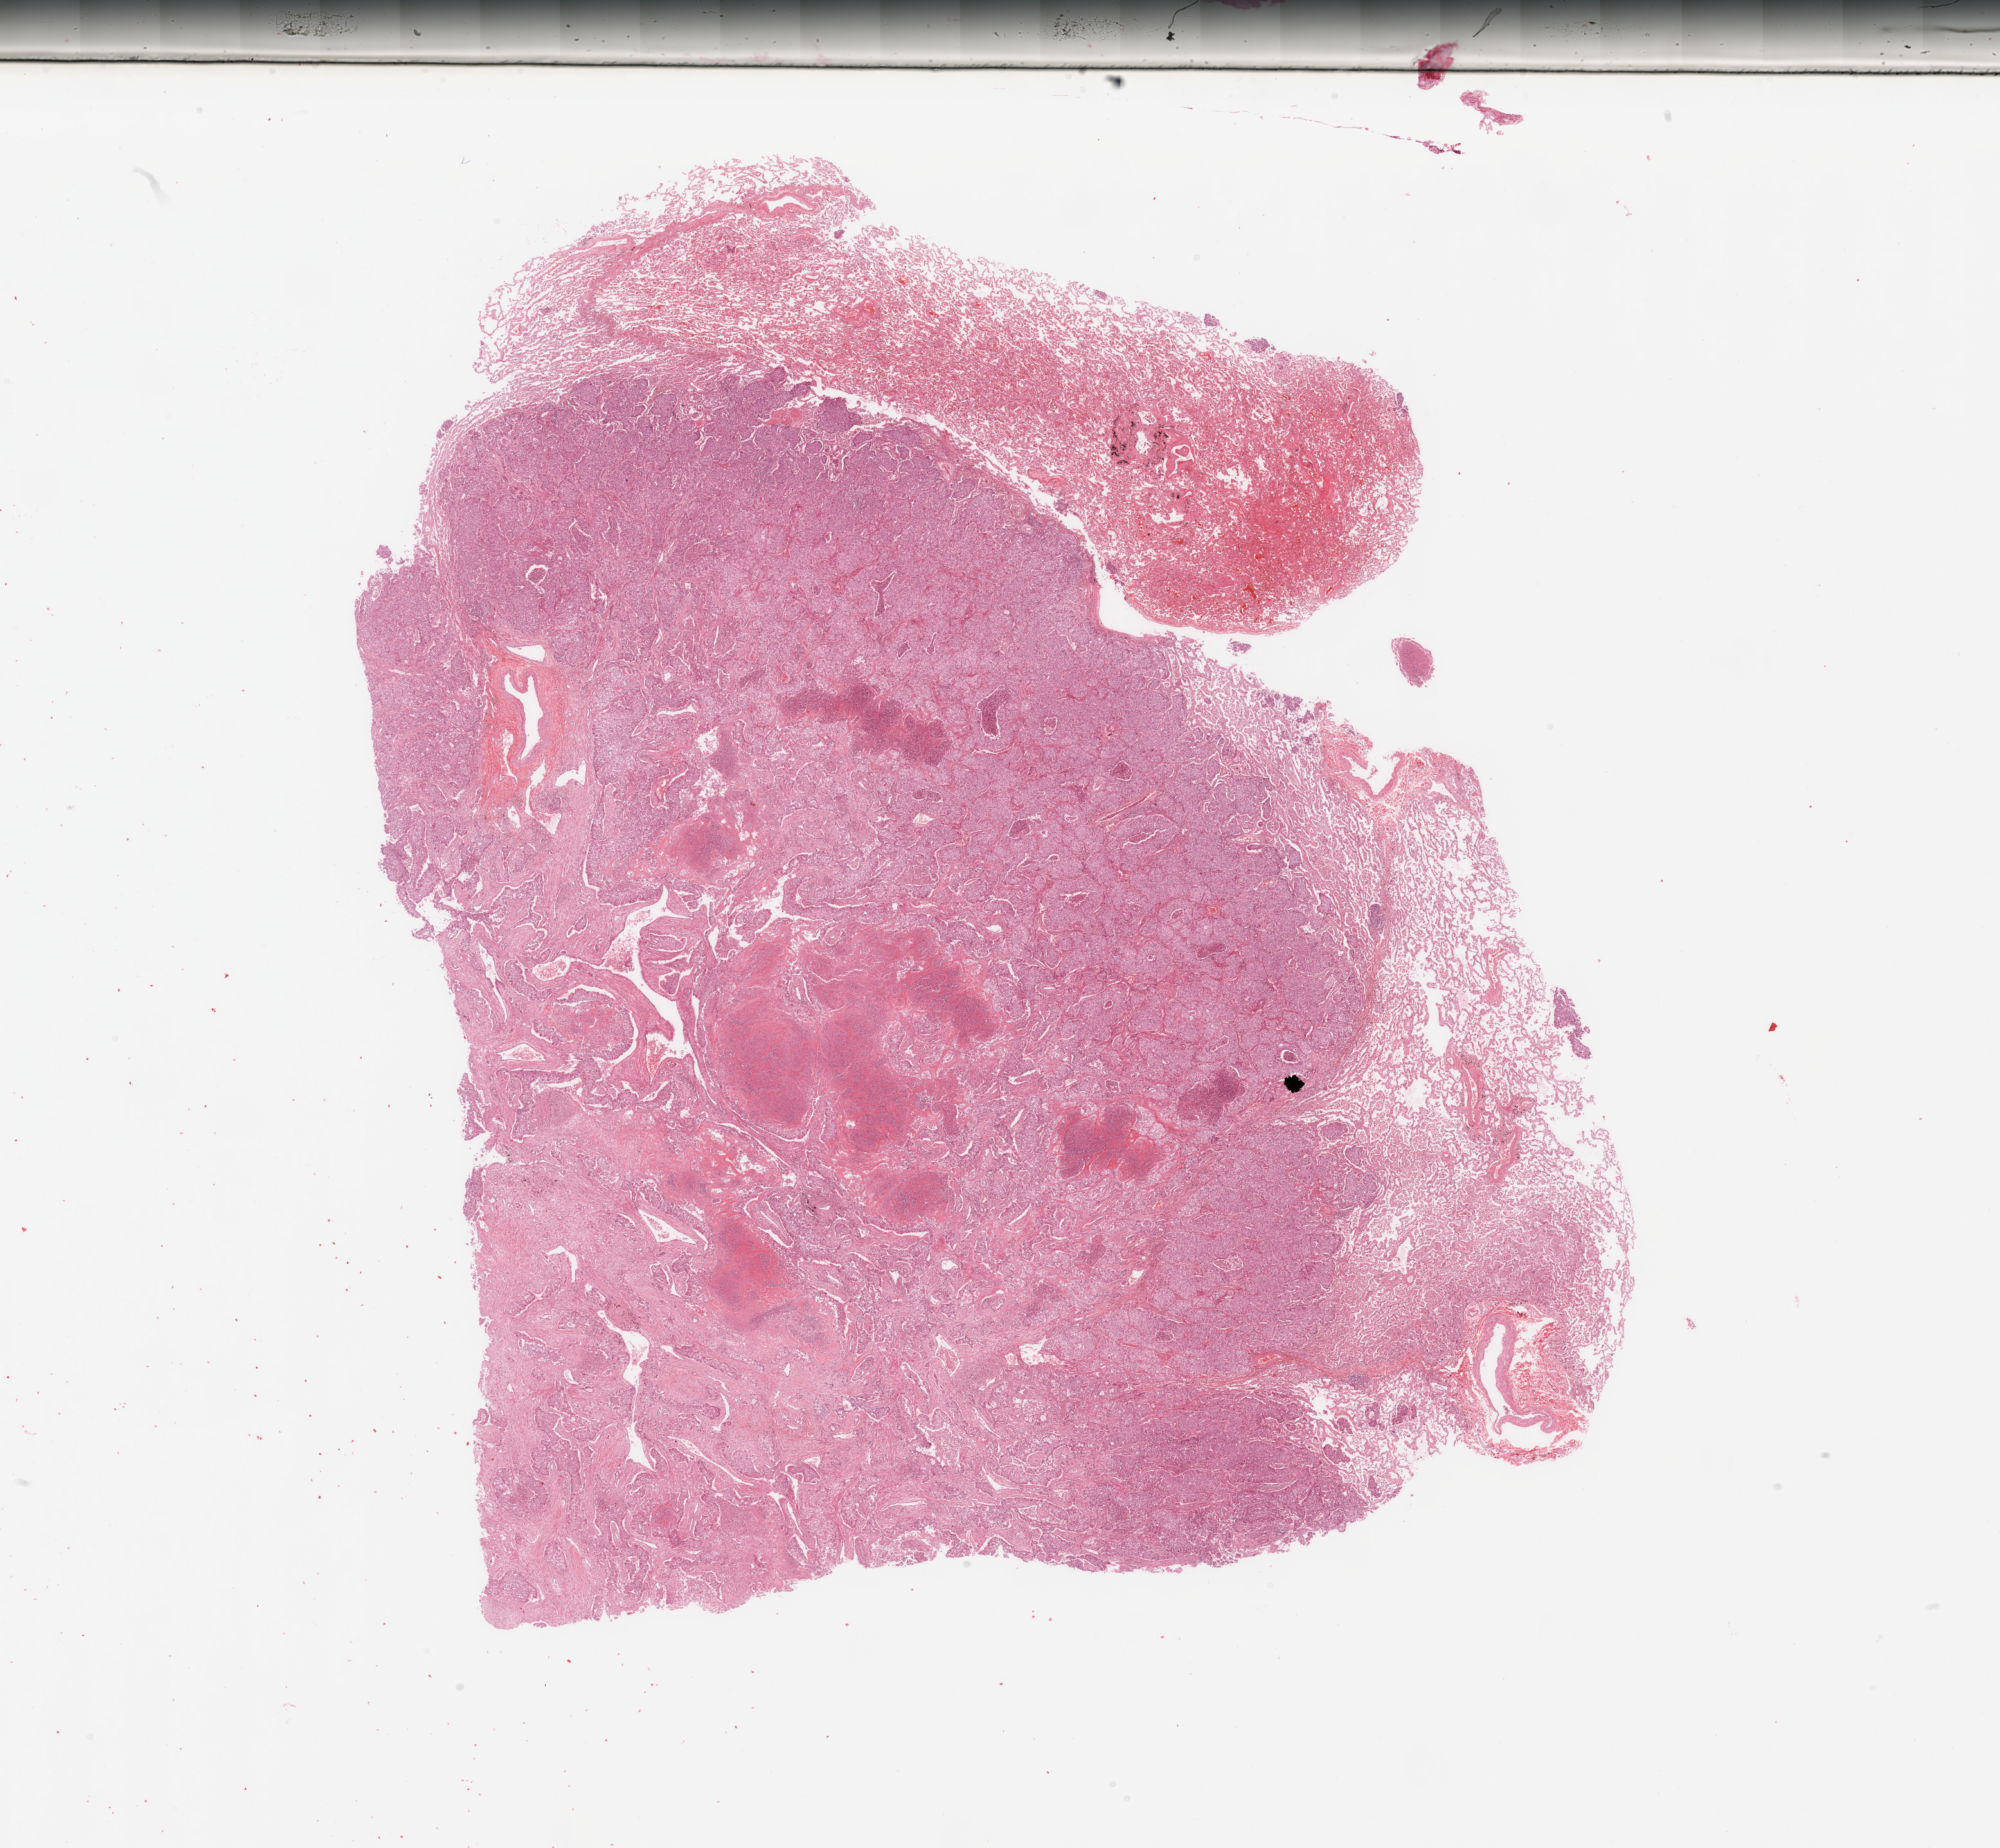
Digitized H&E tissue section (whole slide) — a low-resolution overview of the entire scanned area, about 24.6 x 22.7 mm (from a 20x scan). Tumour tissue sample, sampled site: lung. 57-year-old male patient. Histologic grade: G2 (moderately differentiated). Slide review estimates, as recorded: tumour nuclei 70%, necrosis 15%.
AJCC pathologic stage: IB. Histologic diagnosis: Adenocarcinoma, NOS.